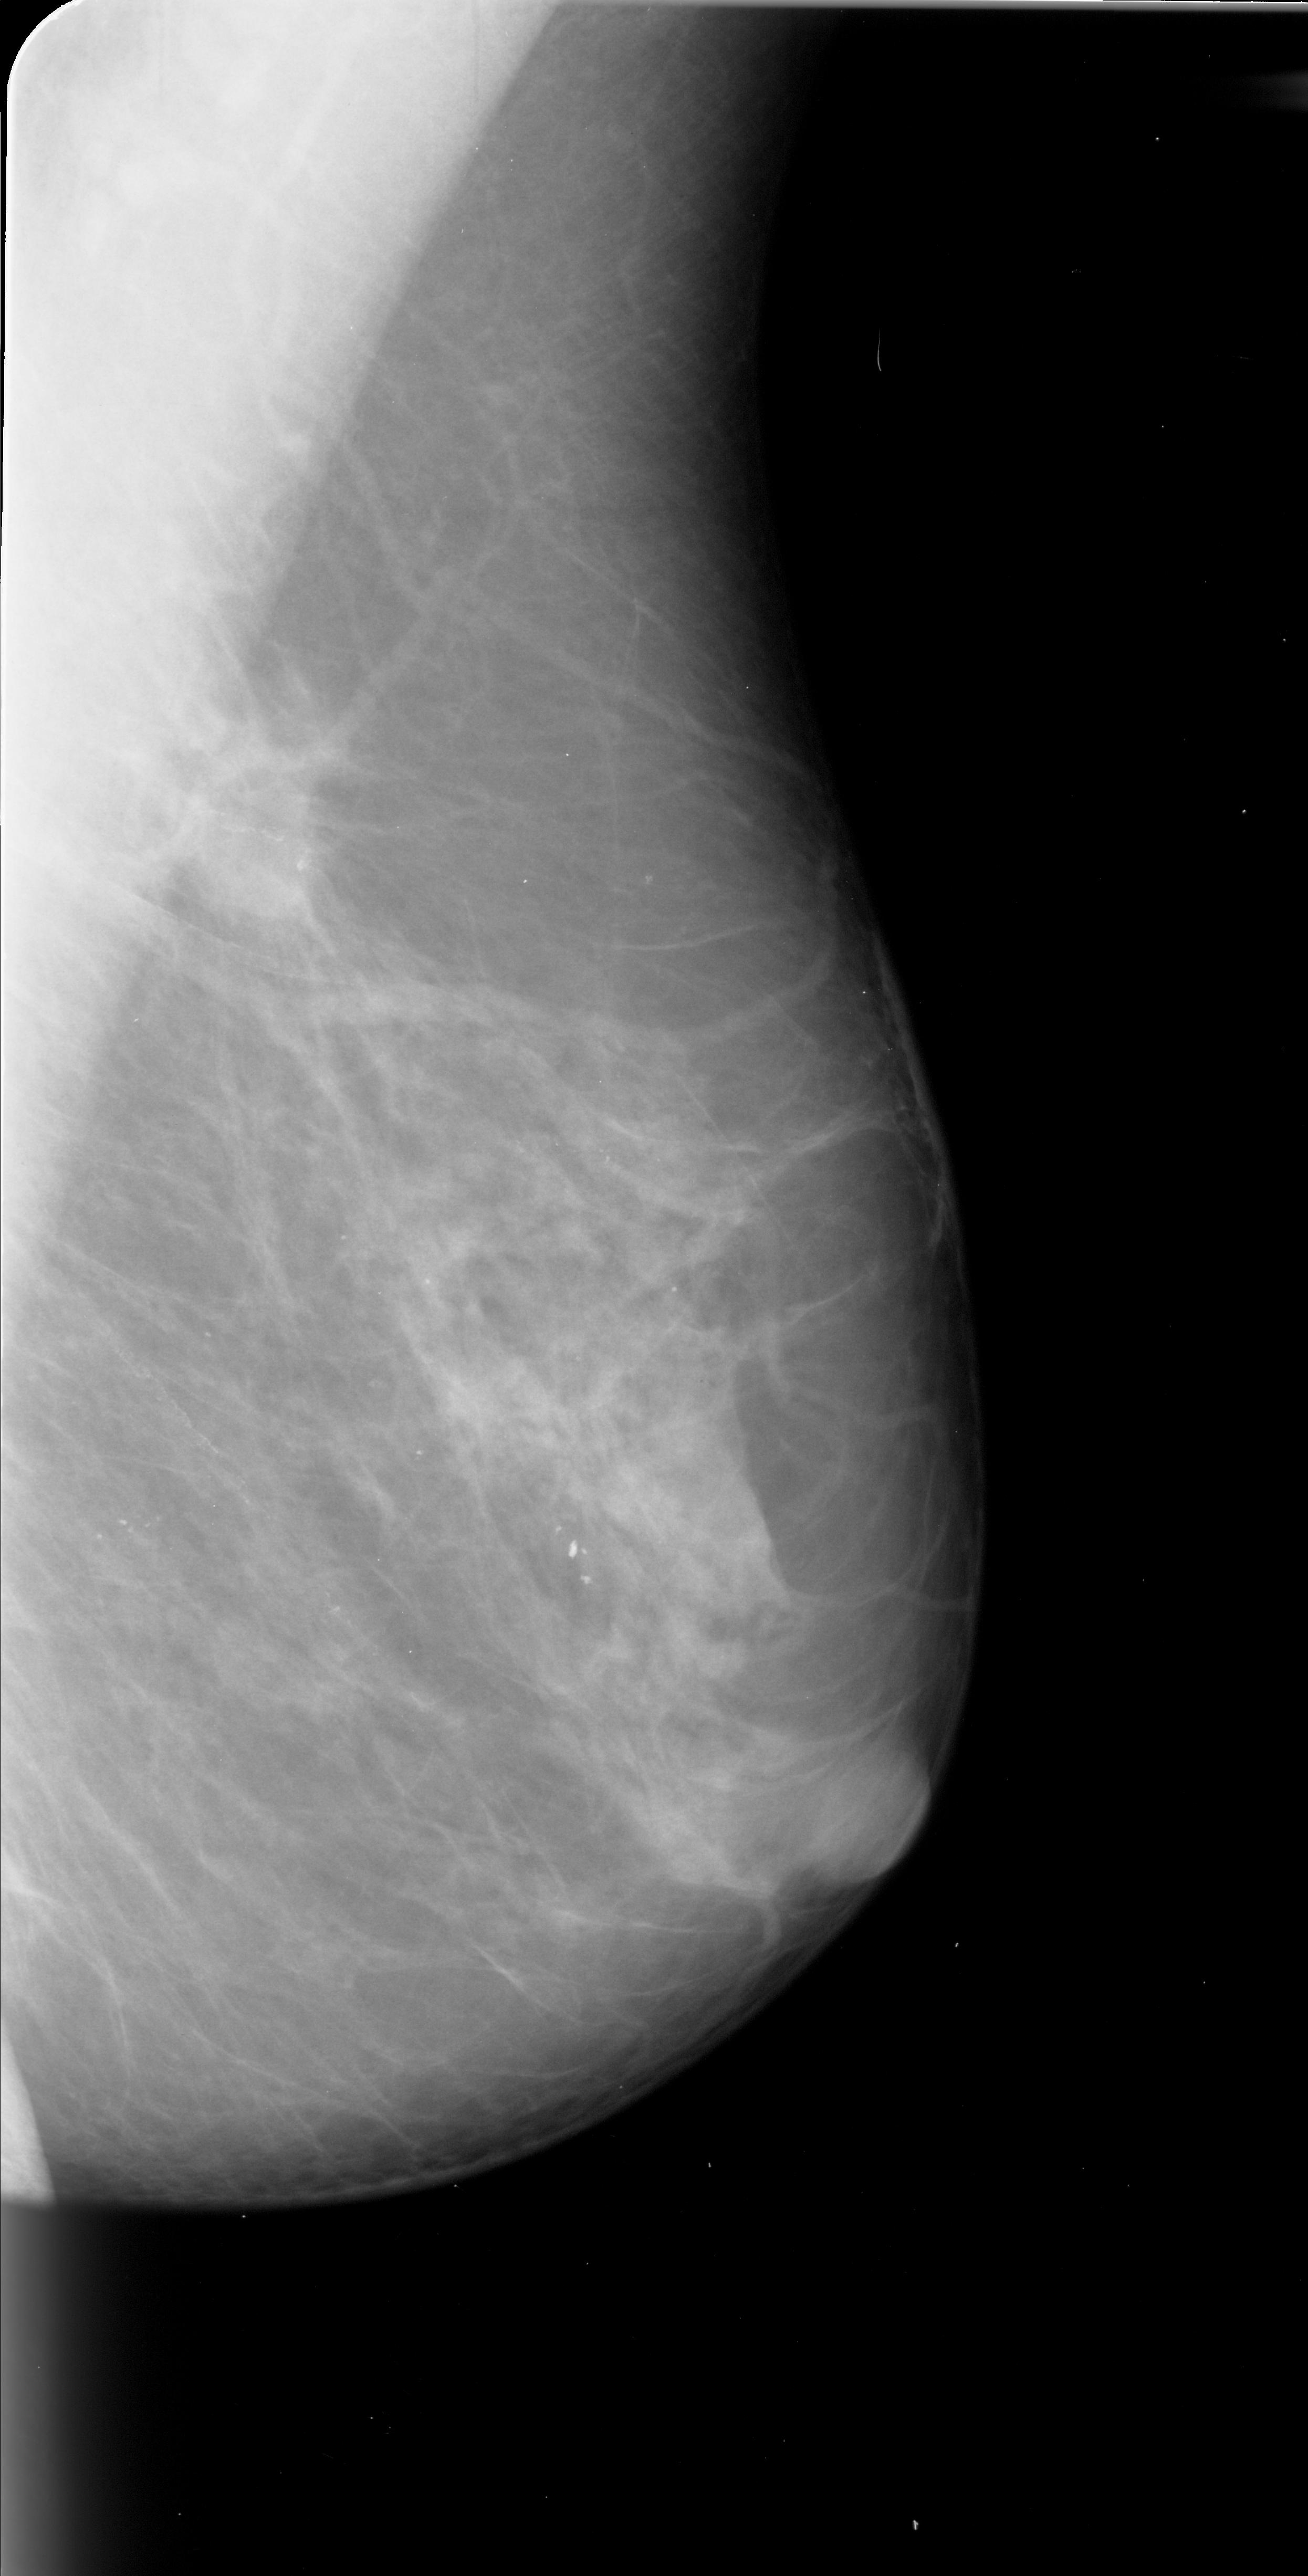
Scanned film-screen mammogram; right breast; MLO view; breast composition: scattered fibroglandular densities (BI-RADS density category 2 of 4).
Mass, shape irregular, margins spiculated; BI-RADS assessment category 5; pathology (as recorded): malignant.